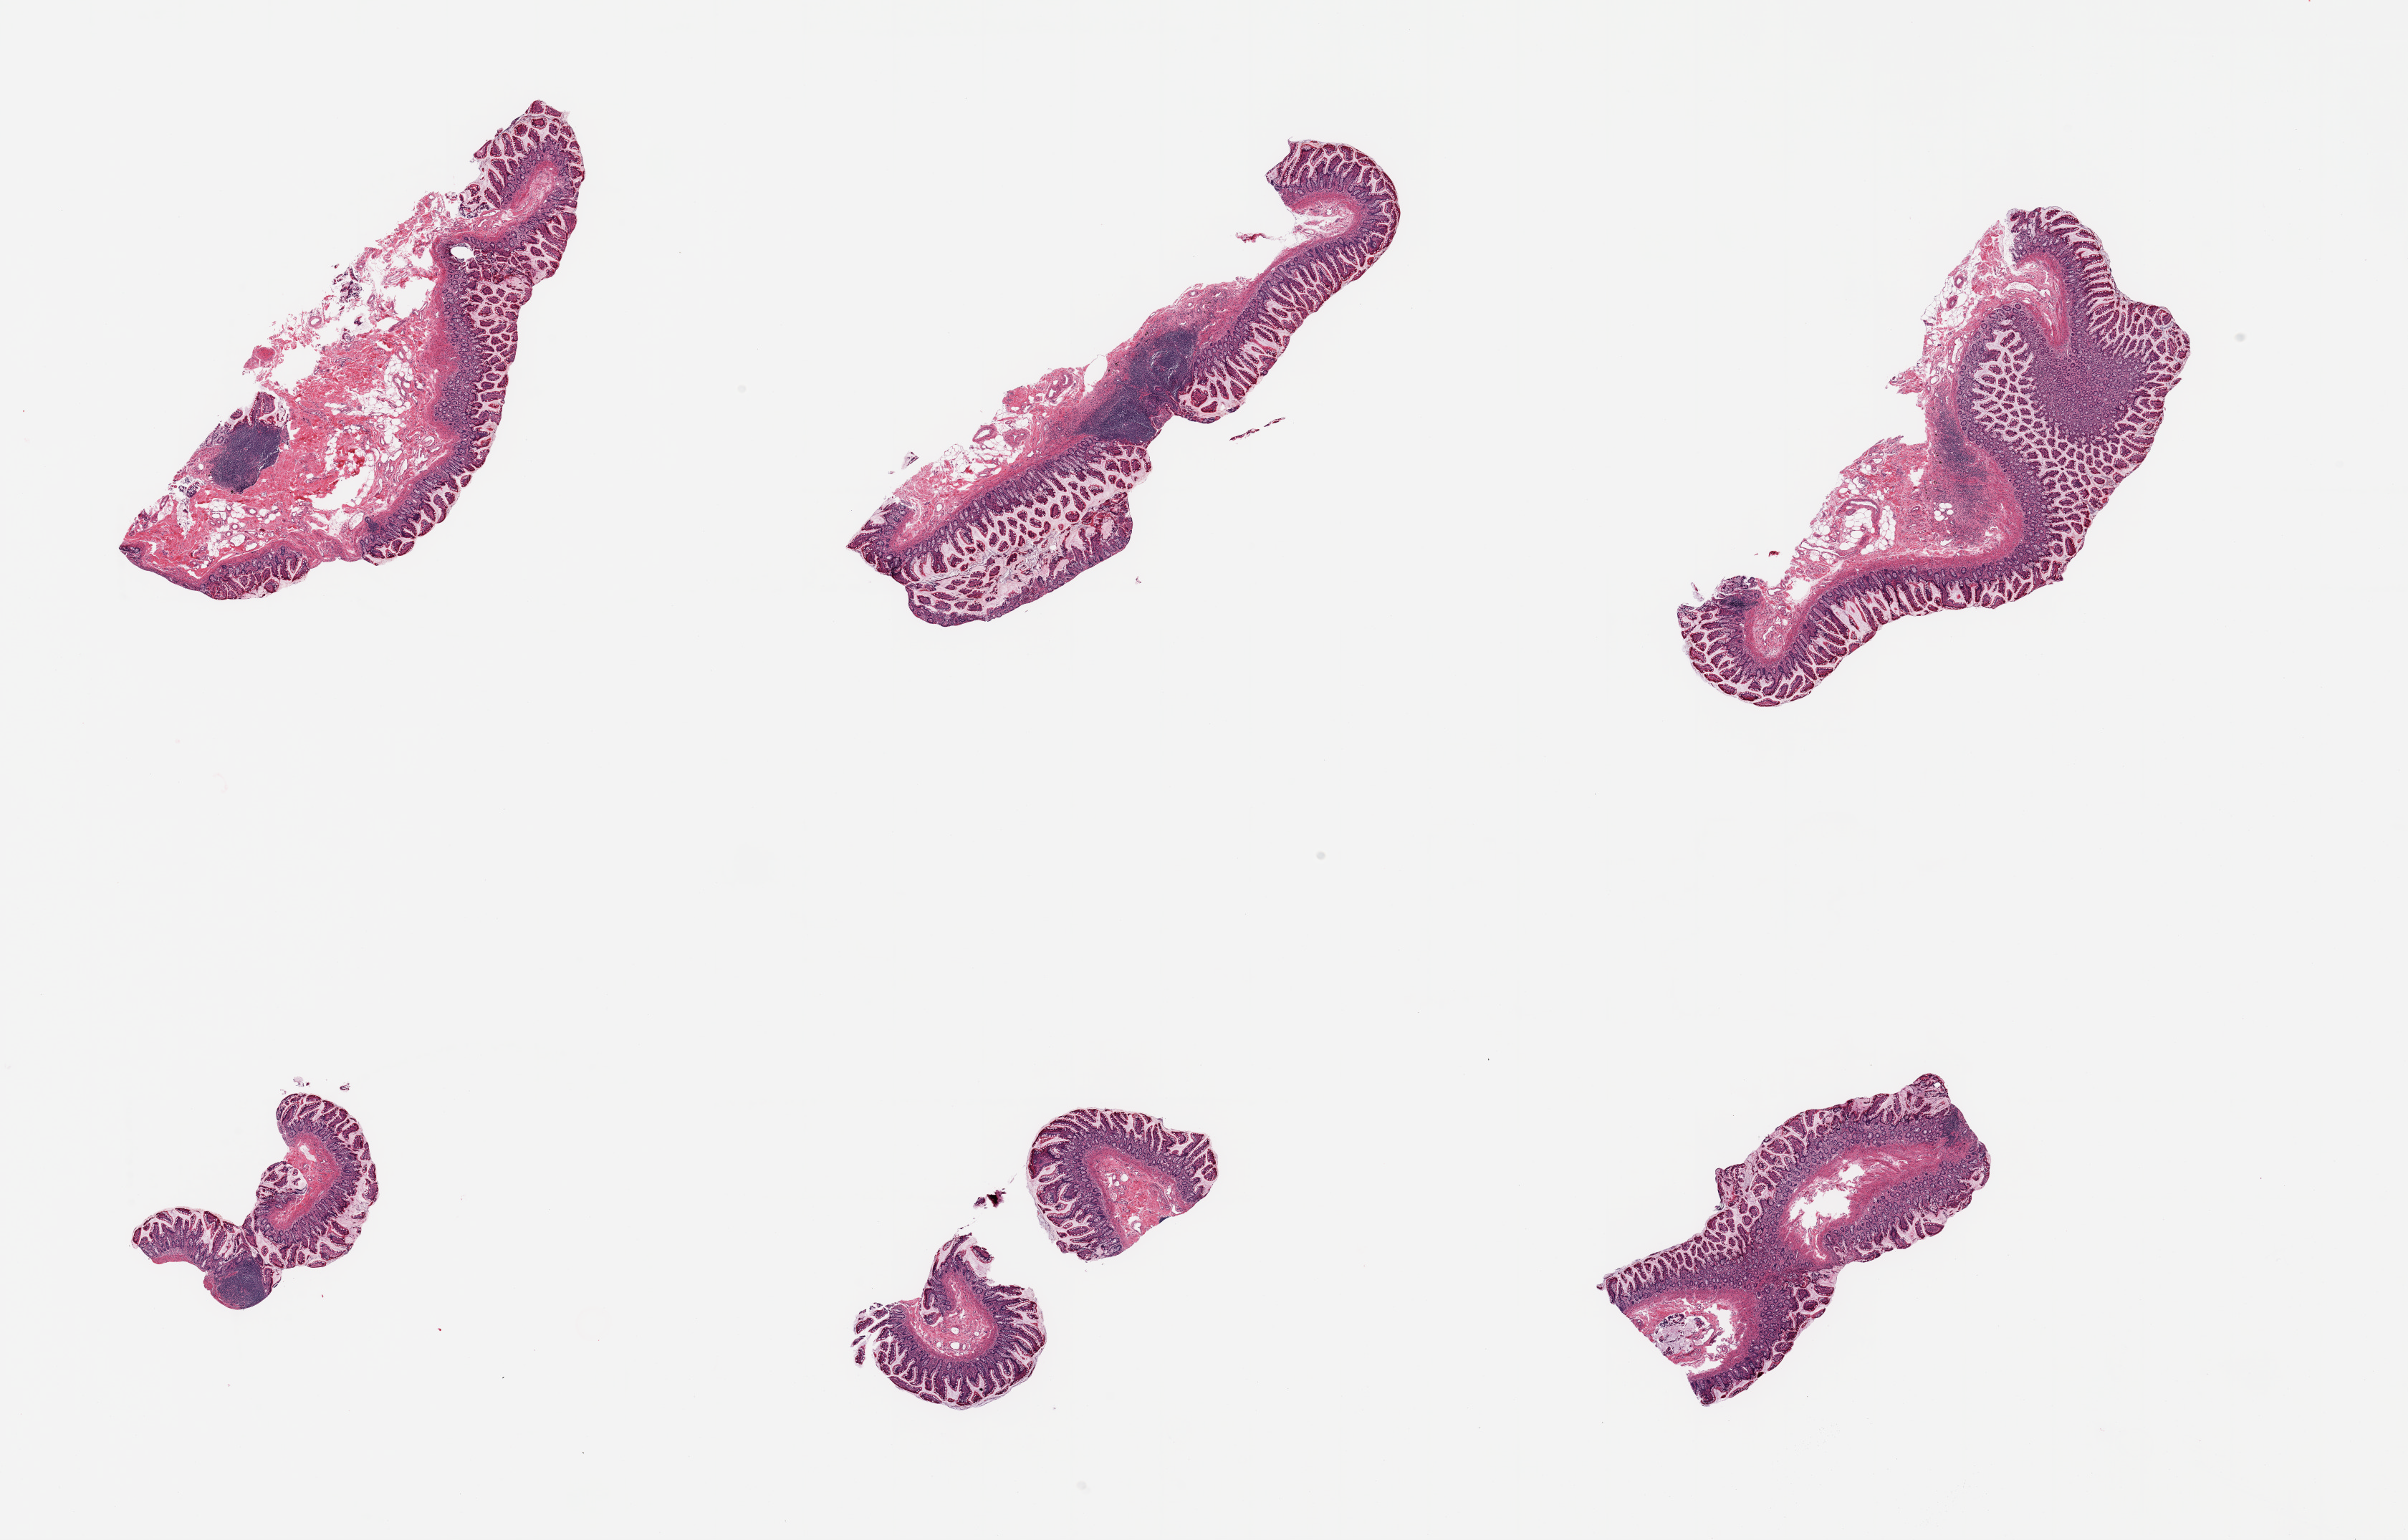
Hematoxylin and eosin (H&E) whole-slide image, low-resolution overview of the scanned area, about 26.6 x 17.0 mm (from a 20x scan). PAXgene-fixed paraffin-embedded (PFPE) section. Section of ileum (target tissue). Donor tissue sample. Donor sex: female.
Pathologist's review note for this sample: 6 pieces, well preserved mucosa, few well preserved target lymphoid aggregates, ~5% total.